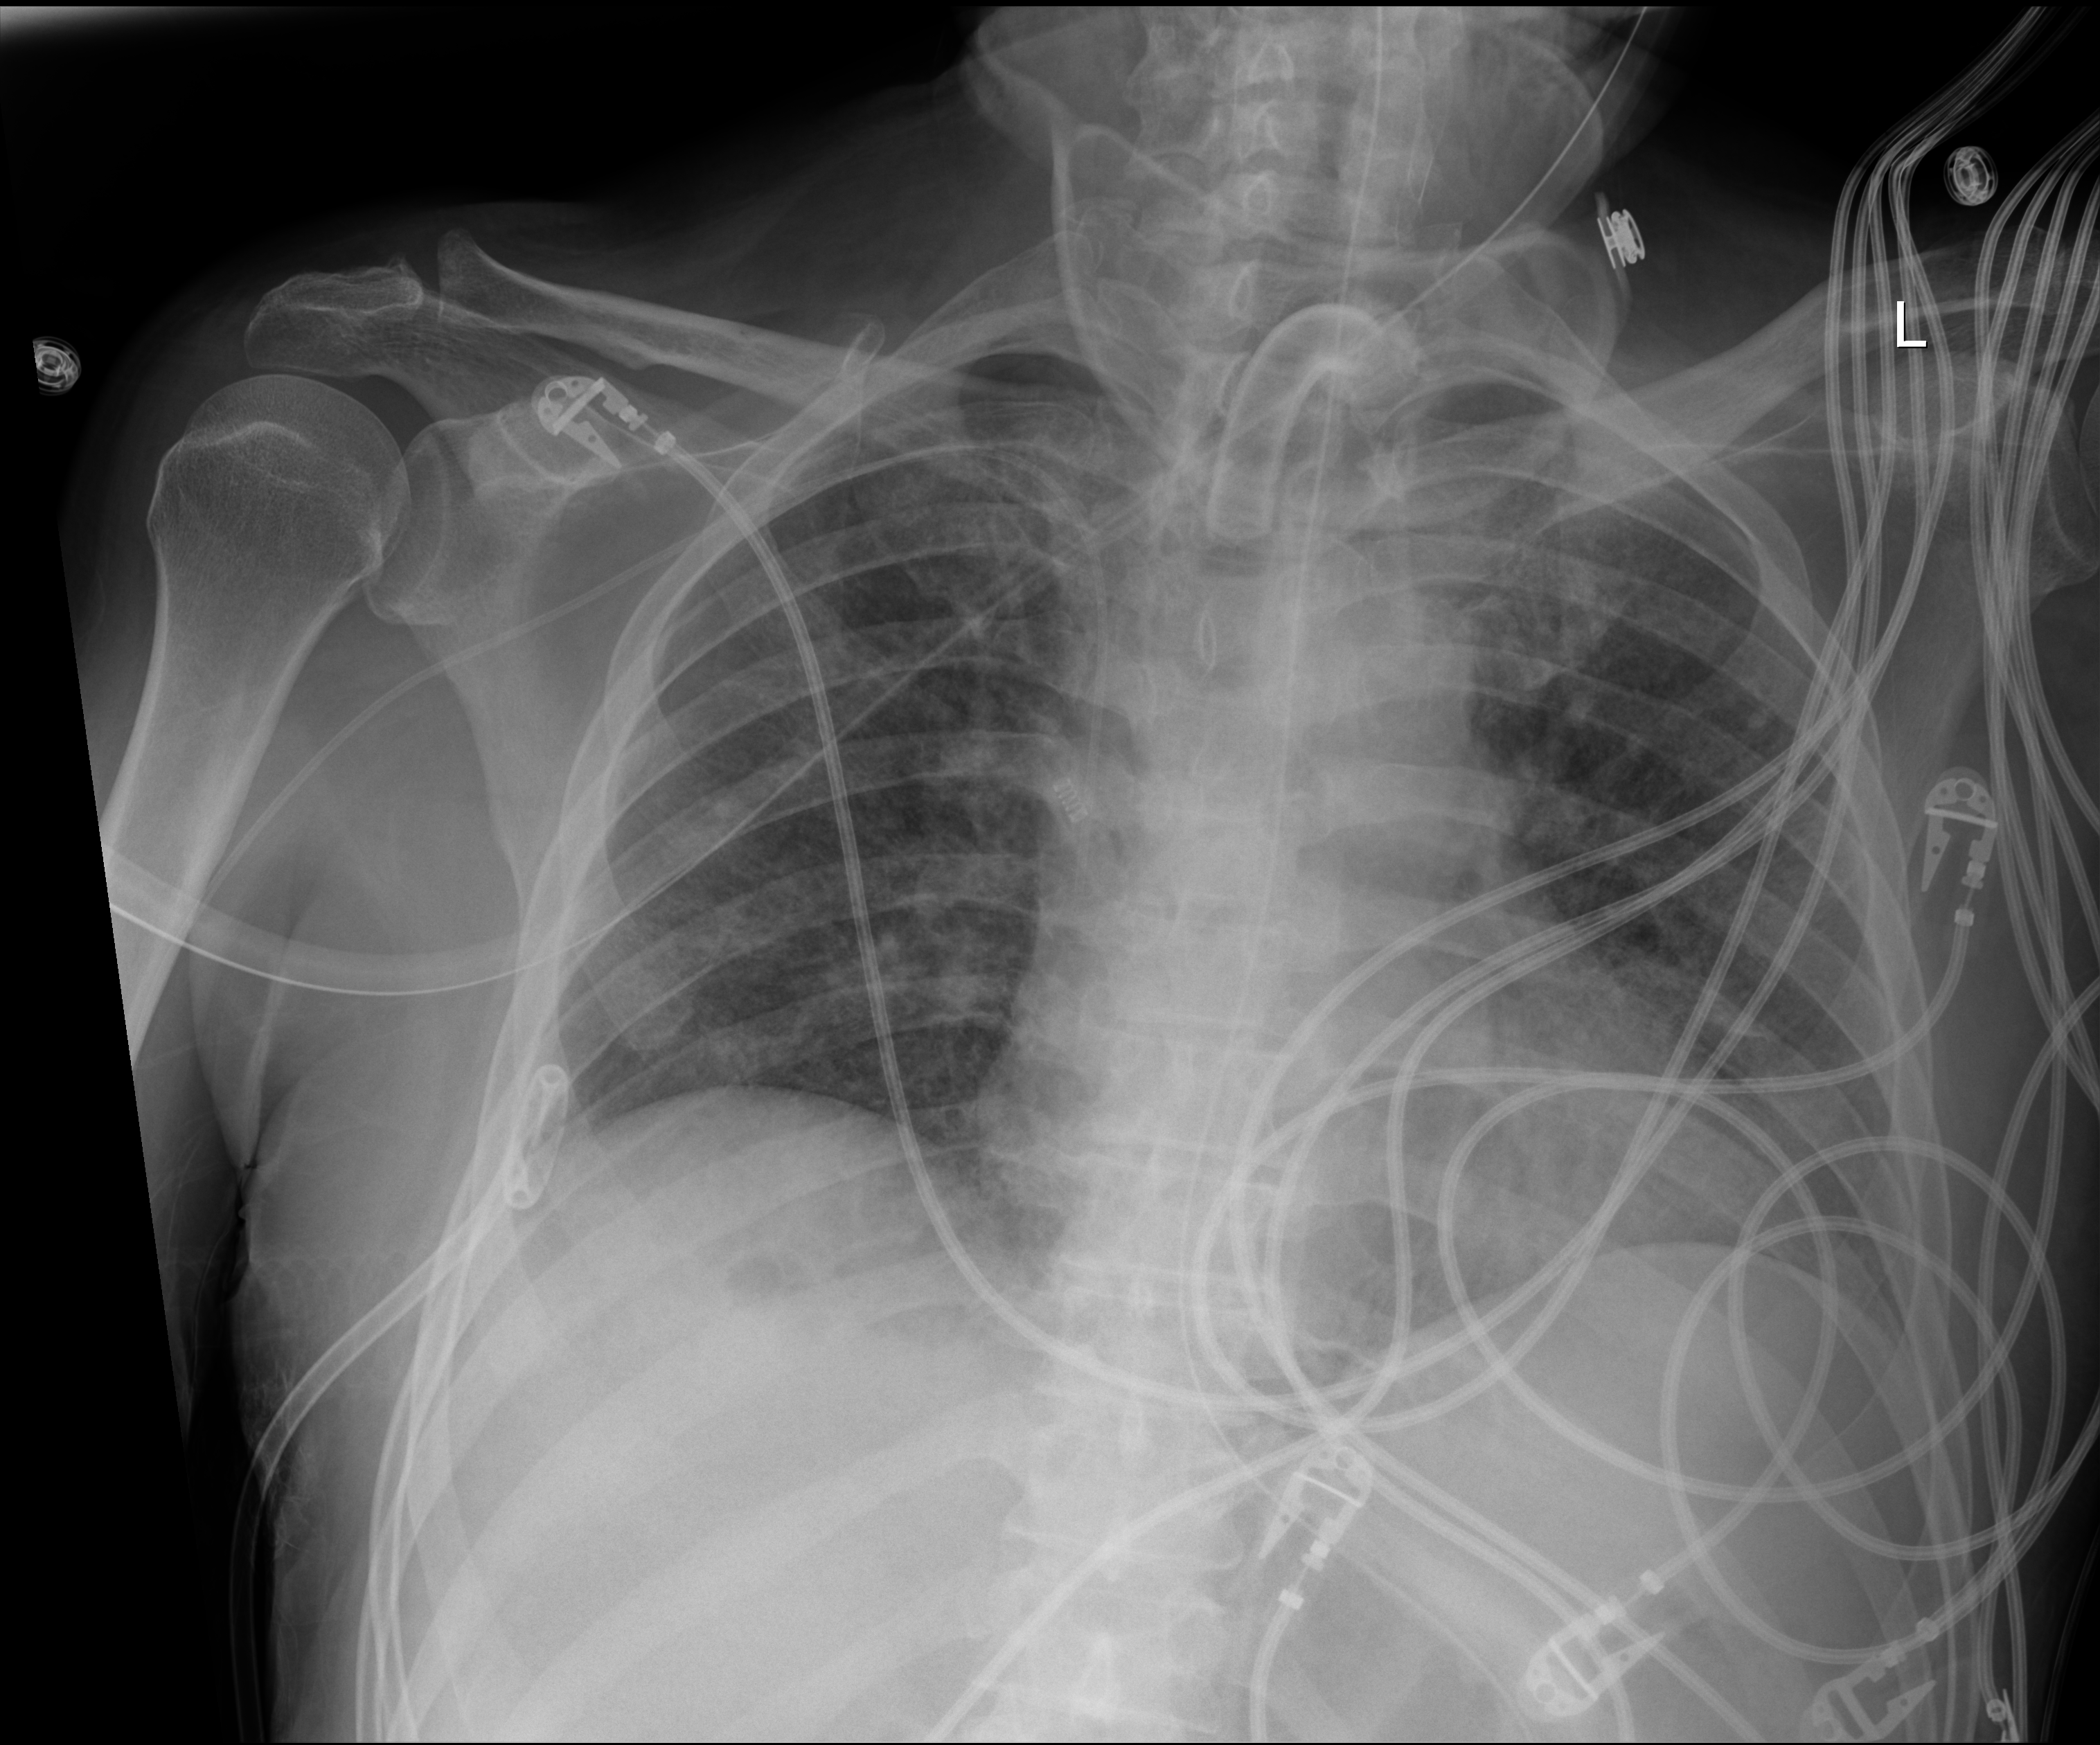
Portable chest radiograph, anteroposterior (AP) projection. Male patient hospitalised with COVID-19, age 18–59 years.
From the hospital-stay record, not from the radiograph (when in the stay this image was taken is not recorded): mechanically ventilated during this hospital stay: yes; admitted to intensive care during this hospital stay: yes; diabetes (admission record): no.